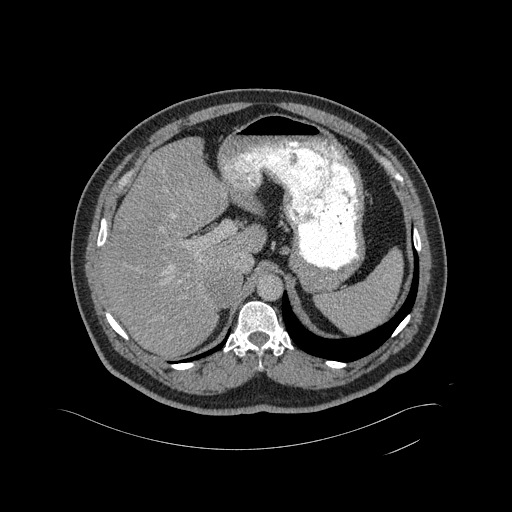
Contrast-enhanced abdominal CT, one axial slice. Position 337 of 433 along the scan axis. 120 kVp. Intravenous contrast given. Soft-tissue window (W 400 / L 40 HU). 2 mm slice thickness. 512 × 512 image matrix, field of view 500 × 500 mm. Patient: male, 56 years. Case-level facts recorded for this patient, not image findings: diagnosis: adrenocortical carcinoma; tumour side: right adrenal; tumour size at pathology: 11.6 cm; Ki-67 index: 50 %; stage (as recorded): 3.
Annotated regions visible in this slice (semi-automatic segmentation, software-assisted and operator-edited):
- mass: box from (x=205, y=269) to (x=240, y=305) px